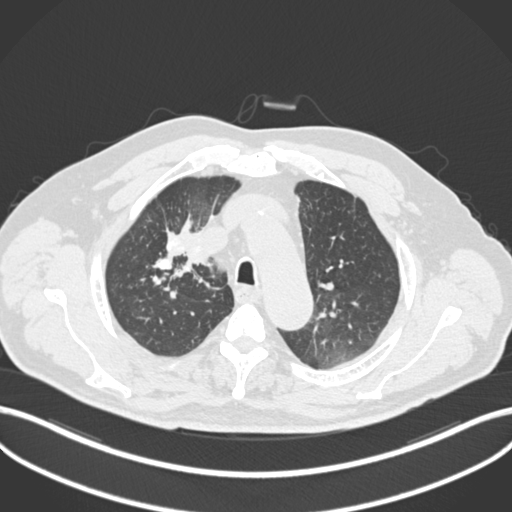
Chest CT, one axial slice; slice 155 of 255 in the series (ordered by position); reconstruction kernel B30f; 120 kVp; lung window (W 1500 / L -600 HU); 1 mm slice thickness; 512 × 512 image matrix. Male patient, age 60 years. Case-level facts recorded for this patient, not image findings: clinical TNM (as recorded): T1b N1 M0.
Structures marked on this image (rectangle marked by the reading radiologist):
- lung tumour (recorded histology: squamous cell carcinoma): bounding box <158,212,224,268> (left, top, right, bottom; pixels)